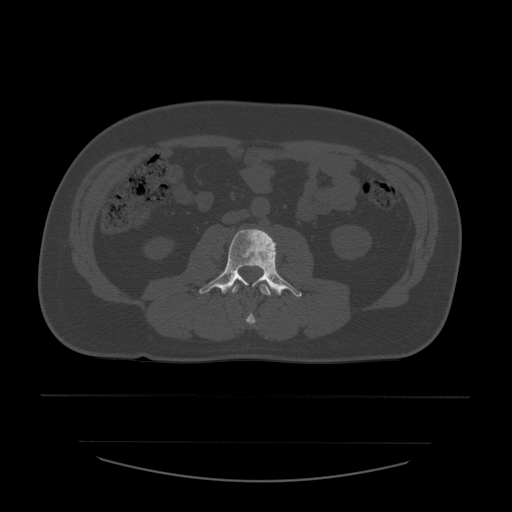
CT including the spine, one axial slice; position 179 of 532 along the scan axis; reconstruction kernel STANDARD; 120 kVp; bone window (W 1800 / L 400 HU); 1.25 mm slice thickness; 512 × 512 image matrix, field of view 441 × 441 mm. Patient age 44 years. Case-level facts recorded for this patient, not image findings: primary cancer: soft tissue sarcoma.
Structures marked on this image (semi-automatically segmented with operator editing):
- L2 vertebra: bounding box (x1, y1, x2, y2) in pixels: (232, 284, 272, 325)
- L3 vertebra: (200, 229, 302, 297)